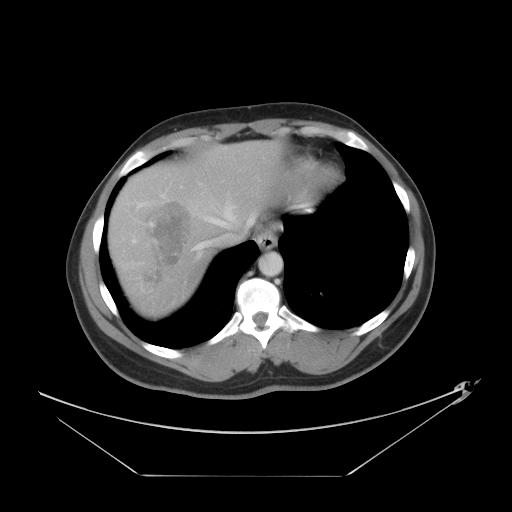
Contrast-enhanced abdominal CT, one axial slice; slice 36 of 44 in the series (ordered by position); reconstruction kernel STANDARD; 120 kVp; intravenous contrast given; soft-tissue window (W 400 / L 40 HU); 5 mm slice thickness; 512 × 512 image matrix, field of view 466 × 466 mm. Male patient, age 49 years. Case-level facts recorded for this patient, not image findings: diagnosis: colorectal cancer liver metastases, imaged before liver resection; multiple liver metastases: no; largest metastasis: 8.5 cm; disease in both lobes: yes.
Structures marked on this image (expert manual segmentation):
- hepatic veins: bounding box [x1, y1, x2, y2] px = [137, 195, 254, 250]
- liver: [107, 140, 289, 319]
- planned liver remnant (the part of the liver to remain after resection): [199, 140, 290, 232]
- portal vein (with intrahepatic branches): [150, 223, 153, 226]
- liver metastasis: [141, 202, 192, 284]